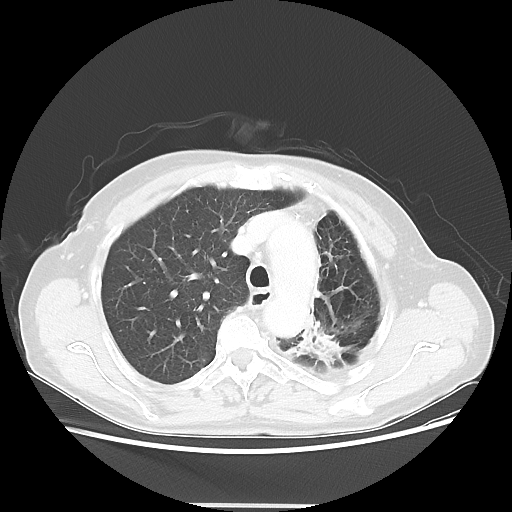
Chest CT, one axial slice; slice 39 of 56 in the series (ordered by position); reconstruction kernel LUNG; 100 kVp; lung window (W 1500 / L -600 HU); 5 mm slice thickness; 512 × 512 image matrix. Patient: female, 63 years. From the clinical record (not read from this slice): clinical TNM (as recorded): T2a N0 M0.
Annotated regions visible in this slice (bounding box drawn by a radiologist):
- lung tumour (recorded histology: adenocarcinoma): bounding box (x1, y1, x2, y2) in pixels: (301, 323, 344, 370)